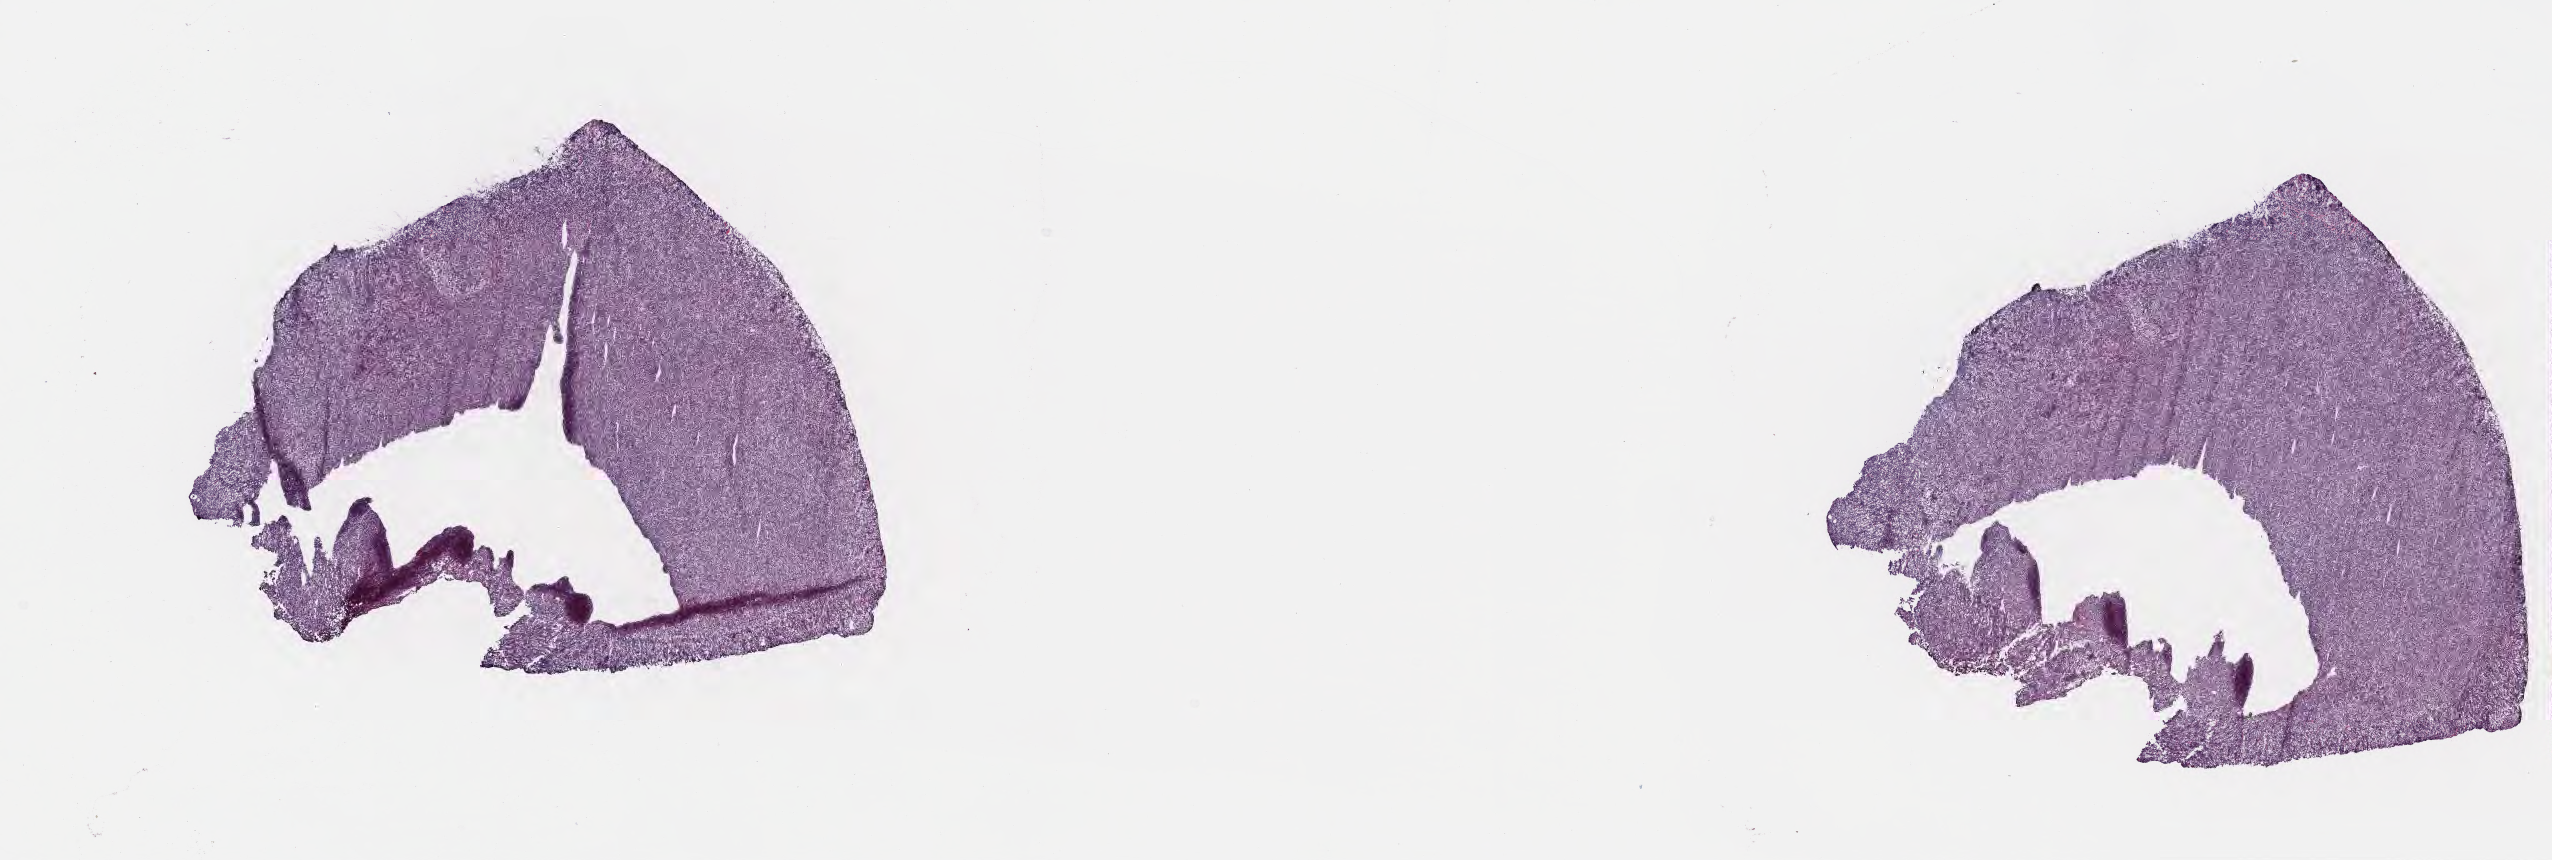
Whole-slide image, haematoxylin and eosin stain, low-resolution overview of the scanned area, about 20.6 x 7.0 mm, frozen section (tissue freezing medium), primary tumor, anatomic site: cranium. Male, age 6 years at initial diagnosis. Slide review estimates, as recorded: tumor cells 100%, tumor nuclei 95%, stromal cells 0%, necrosis 0%, normal cells 0%. Inflammatory infiltration, as recorded: lymphocyte infiltration 40%, monocyte infiltration 40%, neutrophil infiltration 5%.
Ann Arbor stage (patient): Stage I. Diagnosis: Diffuse large B-cell lymphoma, NOS.